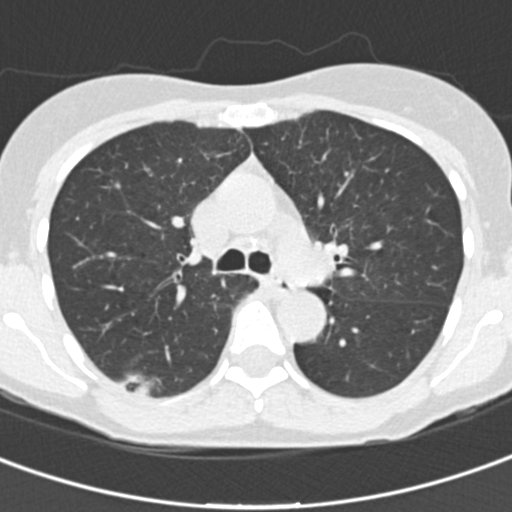
Low-dose screening chest CT, one axial slice. Position 102 of 162 along the scan axis. 120 kVp. Lung window (W 1500 / L -600 HU). 2 mm slice thickness. 512 × 512 image matrix, field of view 276 × 276 mm.
Structures marked on this image (outlined manually by an expert reader):
- lesion 1 (tumor, lower lobe of right lung): bounding box (x1, y1, x2, y2) in pixels: (135, 381, 150, 395)